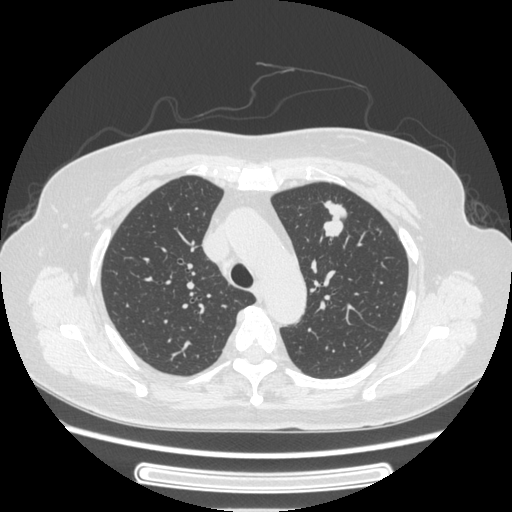
Chest CT, one axial slice. Reconstruction kernel STANDARD. 120 kVp. Lung window (W 1500 / L -600 HU). 1.25 mm slice thickness. 512 × 512 image matrix, field of view 363 × 363 mm. Patient: female, 77 years. Case-level facts recorded for this patient, not image findings: clinical TNM (as recorded): T1c N3 M0.
Structures marked on this image (rectangle marked by the reading radiologist):
- lung tumour (recorded histology: adenocarcinoma): bounding box <317,192,351,250> (left, top, right, bottom; pixels)